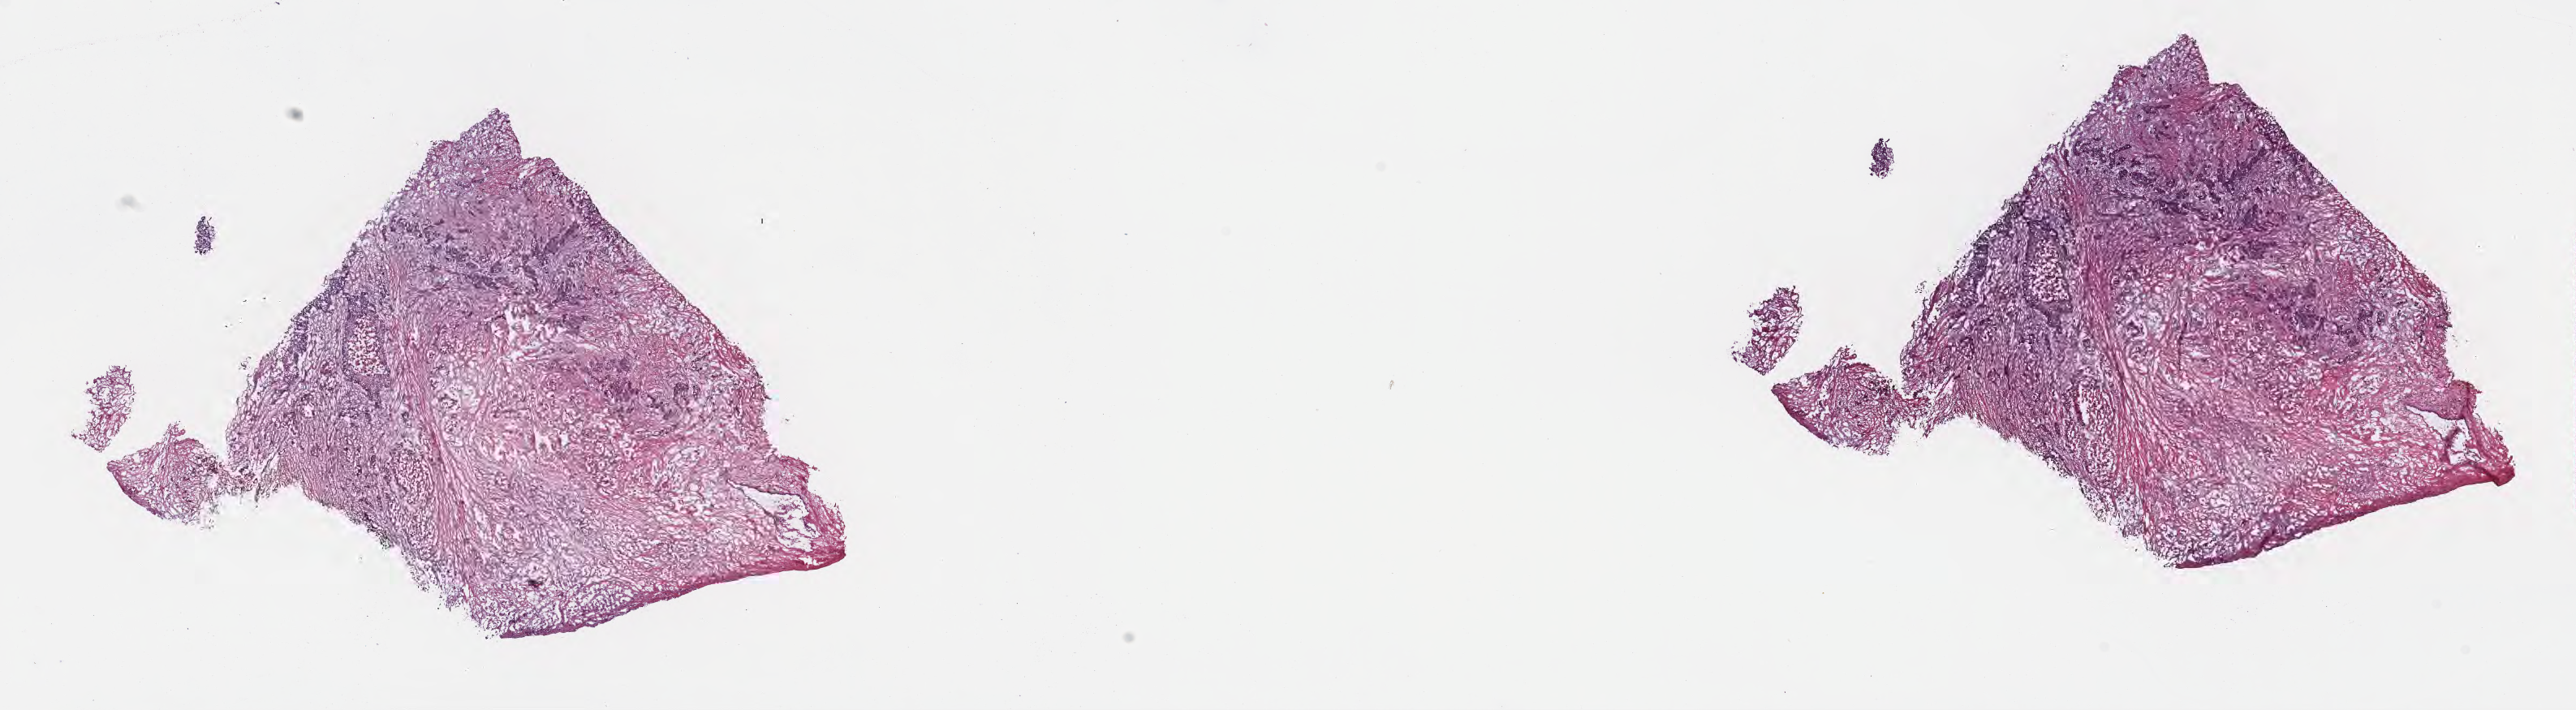
Whole-slide image, H&E stain, shown as a low-resolution overview of the whole scanned area (about 25.7 x 7.1 mm), frozen section, specimen: primary tumor, site: head of pancreas. Female, age 64 years at initial diagnosis. Tumor grade: G3 (poorly differentiated). Pathologist review of this section (percent, as recorded): tumor cells 20%, tumor nuclei 85%, stromal cells 80%, necrosis 0%, normal cells 0%. Inflammatory infiltration, as recorded: lymphocyte infiltration 0%, monocyte infiltration 0%, neutrophil infiltration 0%.
AJCC pathologic stage: Stage III. Section: bottom of the tissue portion. Histologic diagnosis: Infiltrating duct carcinoma, NOS.